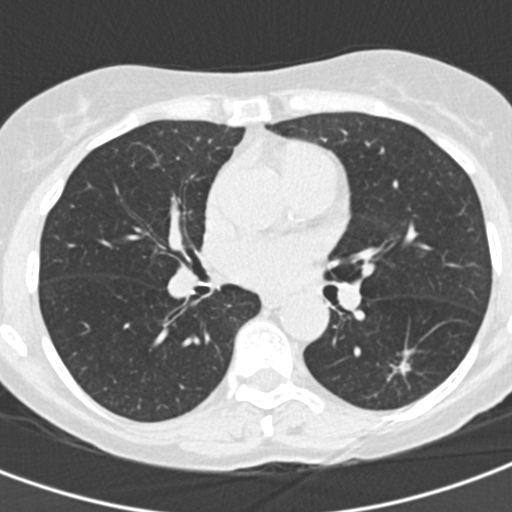
Low-dose screening chest CT, one axial slice; position 82 of 155 along the scan axis; reconstruction kernel B30f; 120 kVp; lung window (W 1500 / L -600 HU); 512 × 512 image matrix, field of view 282 × 282 mm.
Structures marked on this image (manually delineated by an expert):
- lesion 1 (tumor, lower lobe of left lung): bounding box [x1, y1, x2, y2] px = [387, 359, 412, 382]